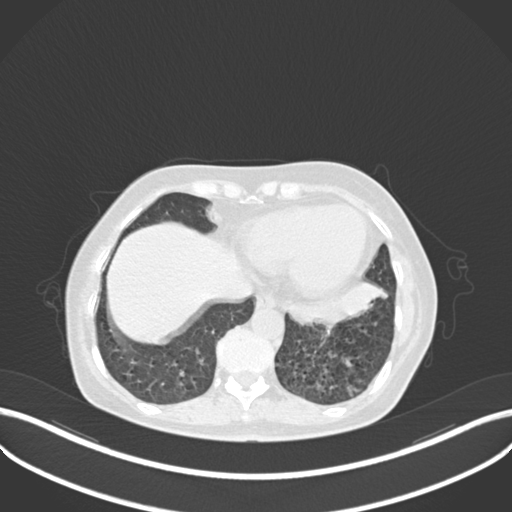
Chest CT, one axial slice. Position 63 of 270 along the scan axis. Reconstruction kernel B30f. Lung window (W 1500 / L -600 HU). 1 mm slice thickness. 512 × 512 image matrix, field of view 400 × 400 mm. Patient: female, 63 years. Case-level facts recorded for this patient, not image findings: clinical TNM (as recorded): T1b N0 M0; histopathological grade: G2-3.
Outlined on this slice (bounding box drawn by a radiologist):
- lung tumour (recorded histology: adenocarcinoma): bounding box [x1, y1, x2, y2] px = [288, 274, 390, 329]